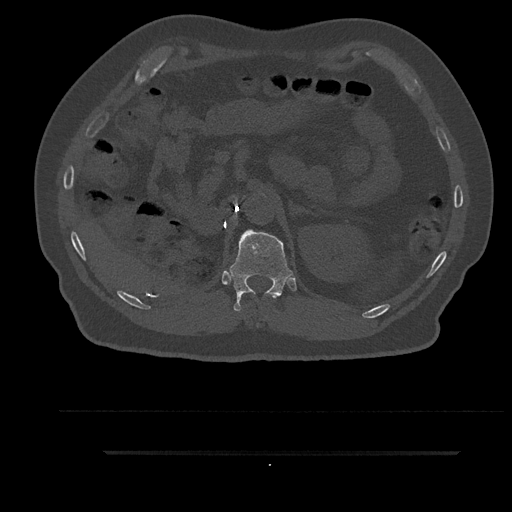
CT including the spine, one axial slice; position 255 of 797 along the scan axis; 120 kVp; bone window (W 1800 / L 400 HU); 512 × 512 image matrix, field of view 432 × 432 mm. Patient: male, 63 years. From the clinical record (not read from this slice): primary cancer: renal; vertebrae with lytic lesions (as recorded): T8.
Structures marked on this image (semi-automatic segmentation, software-assisted and operator-edited):
- T11 vertebra: bounding box <272,296,277,298> (left, top, right, bottom; pixels)
- T12 vertebra: <227,229,293,311>